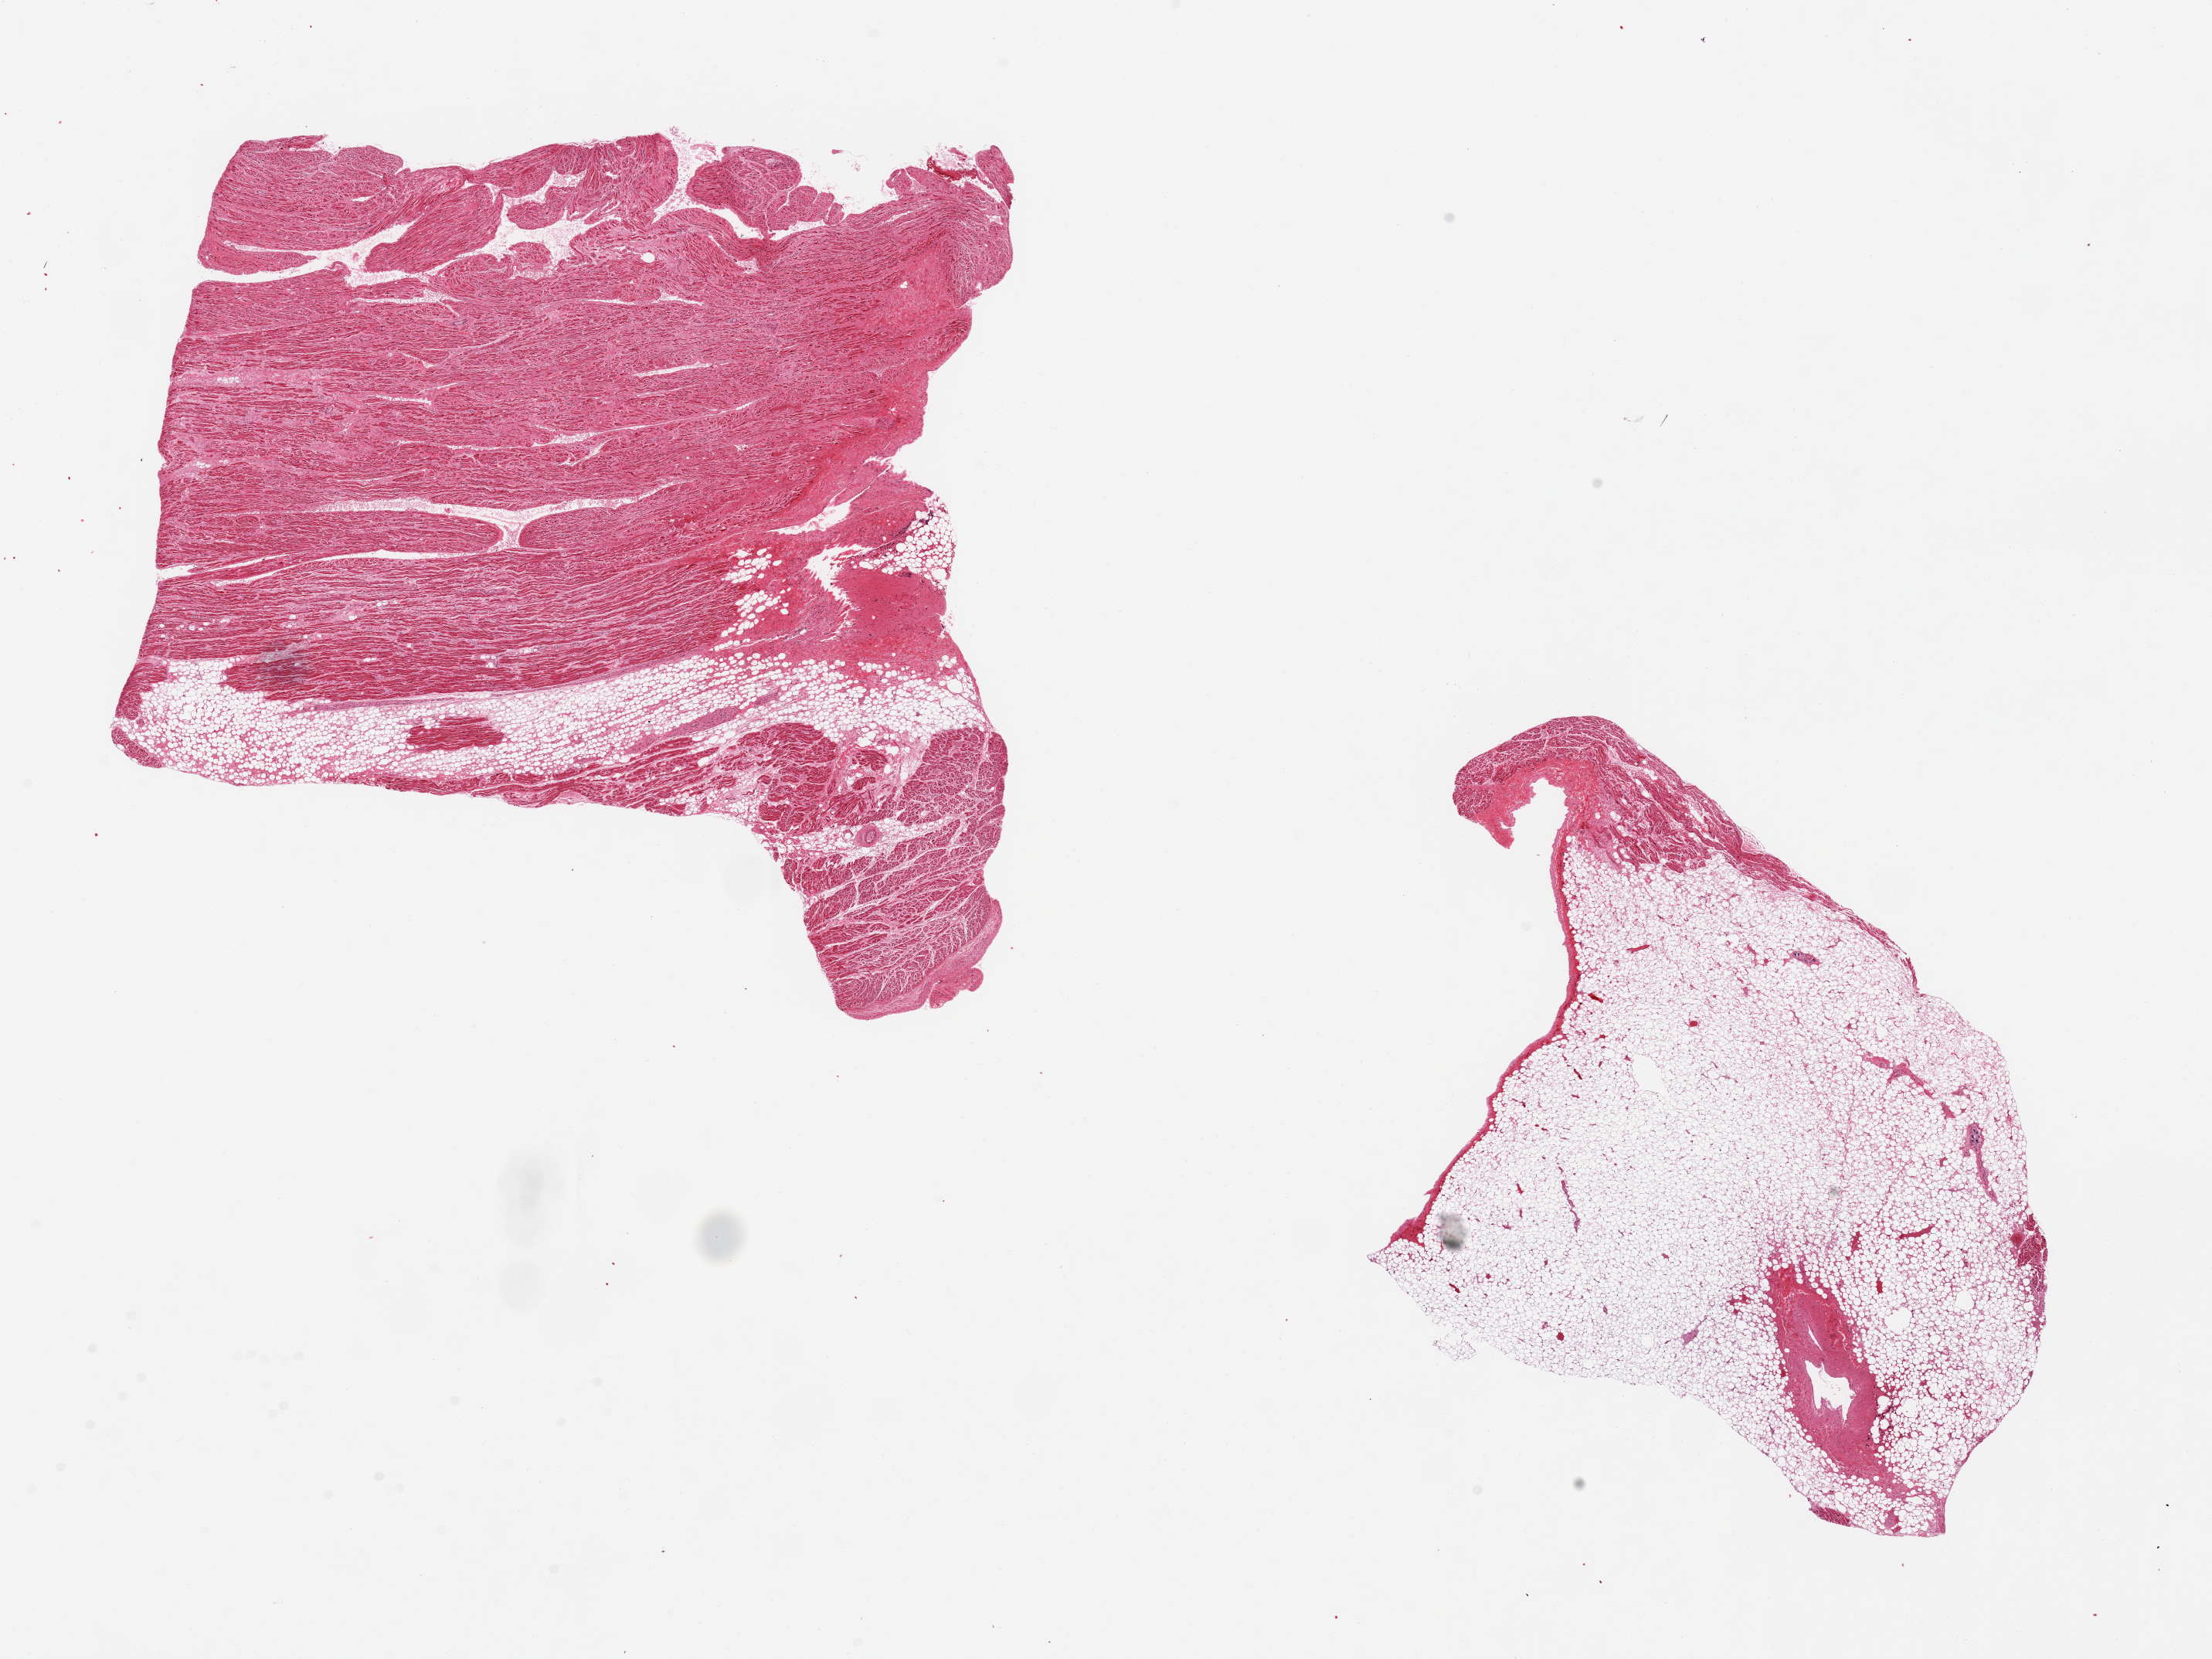
Digitized hematoxylin and eosin (H&E)-stained section, brightfield, low-resolution overview of the scanned area, about 22.6 x 17.0 mm. PAXgene-fixed, paraffin-embedded tissue. Section of auricular appendage (target tissue). Tissue donor sample. Donor: male.
Reviewer comment on this tissue sample: 2 pieces; 1 has 10% fat, other is 90% external fat.